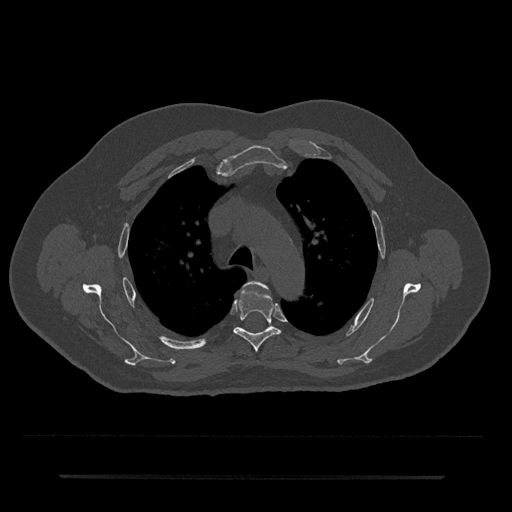
CT including the spine, one axial slice; slice 527 of 797 in the series (ordered by position); 120 kVp; bone window (W 1800 / L 400 HU); 512 × 512 image matrix. Patient: male, 69 years. From the clinical record (not read from this slice): primary cancer: prostate.
Outlined on this slice (semi-automatically segmented with operator editing):
- T3 vertebra: box from (x=244, y=282) to (x=267, y=288) px
- T4 vertebra: (x=233, y=289)–(x=281, y=352)